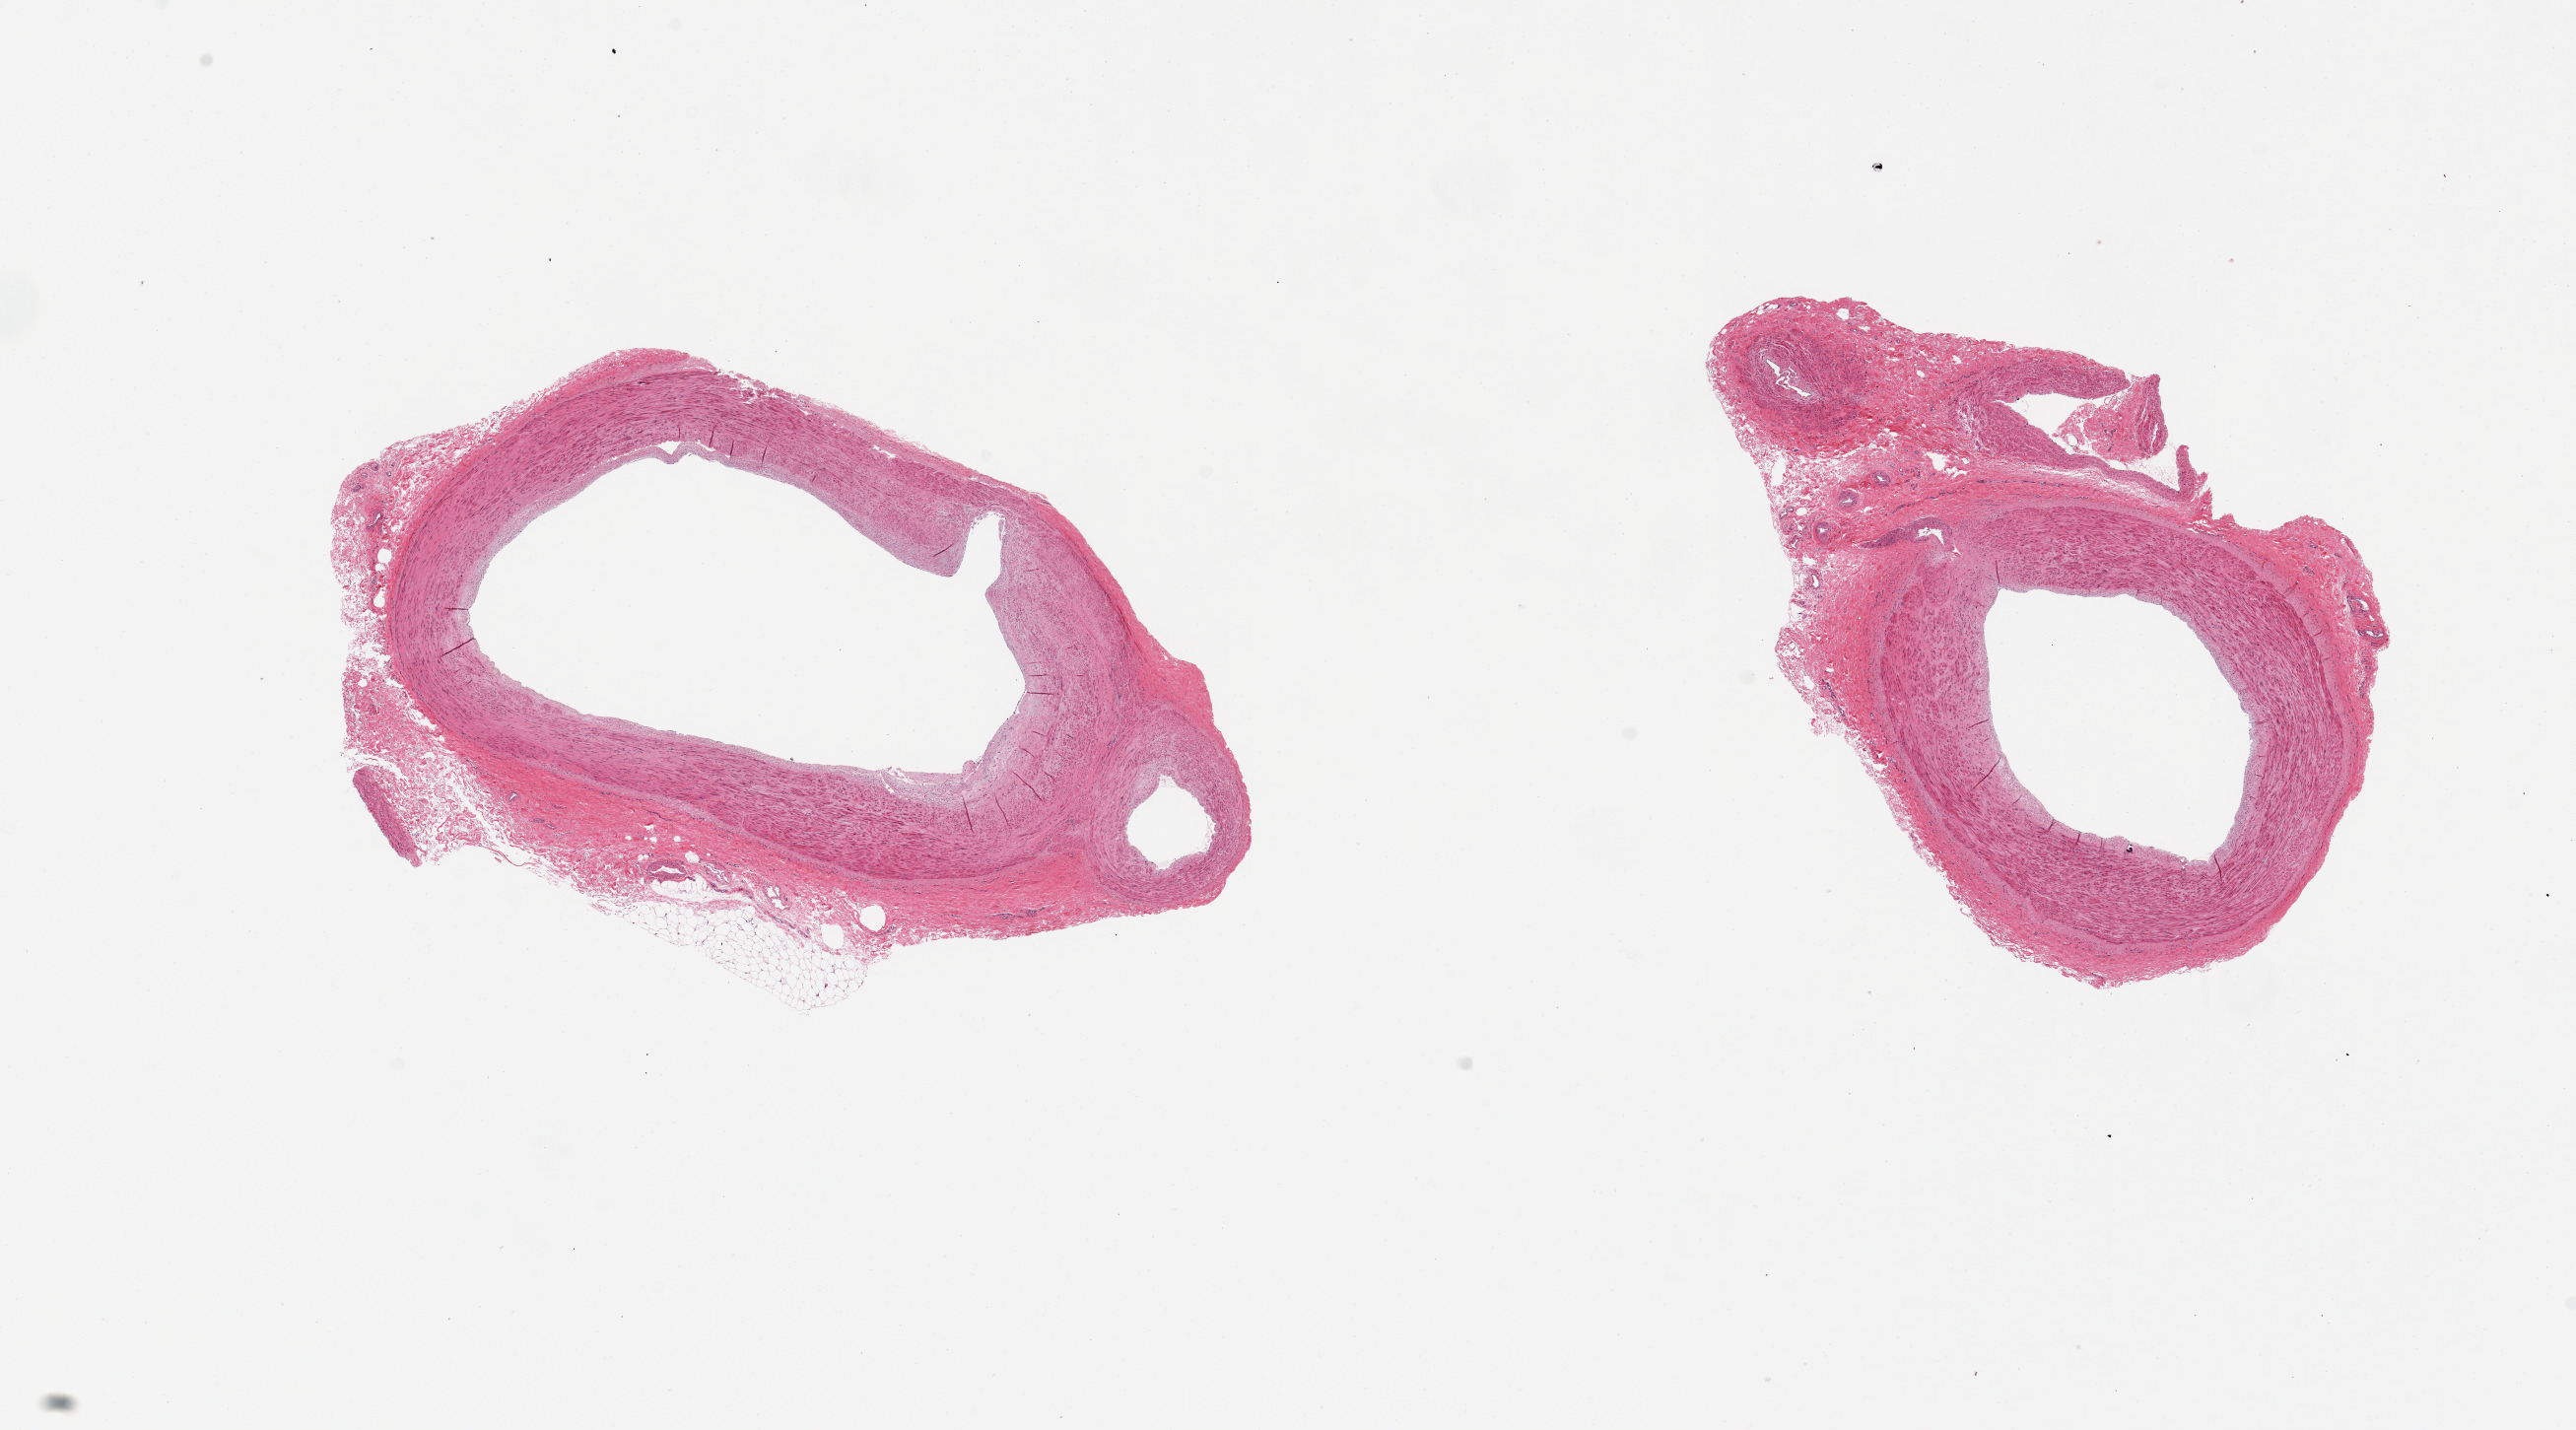
H&E whole-slide image, shown as a low-resolution overview of the whole scanned area (about 20.7 x 11.5 mm); PAXgene-fixed paraffin-embedded (PFPE) section; sampled site (target tissue): tibial artery; tissue donor sample. Donor sex: female.
Reviewer comment on this tissue sample: 2 pieces, 8x5 & 6.5x4mm. Well trimmed, minimal adventitial stroma. Each piece has a large and a small artery.